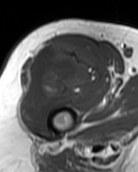
MRI of an extremity soft-tissue mass, one axial slice. Slice 70 of 99 in the series (ordered by position). MR volume resampled by the dataset authors to the PET/CT grid (not the native acquisition matrix). 3.27 mm slice thickness. 138 × 172 image matrix. Female patient. Case-level facts recorded for this patient, not image findings: histological type: pleiomorphic undifferentiated sarcoma; grade: high; site of the primary tumour: right quadricep.
Structures marked on this image (expert contour drawn on MRI and transferred to this co-registered scan by the dataset authors):
- gross tumour volume including surrounding oedema: bounding box <21,39,104,122> (left, top, right, bottom; pixels)
- gross tumour volume (mass): <21,39,104,122>